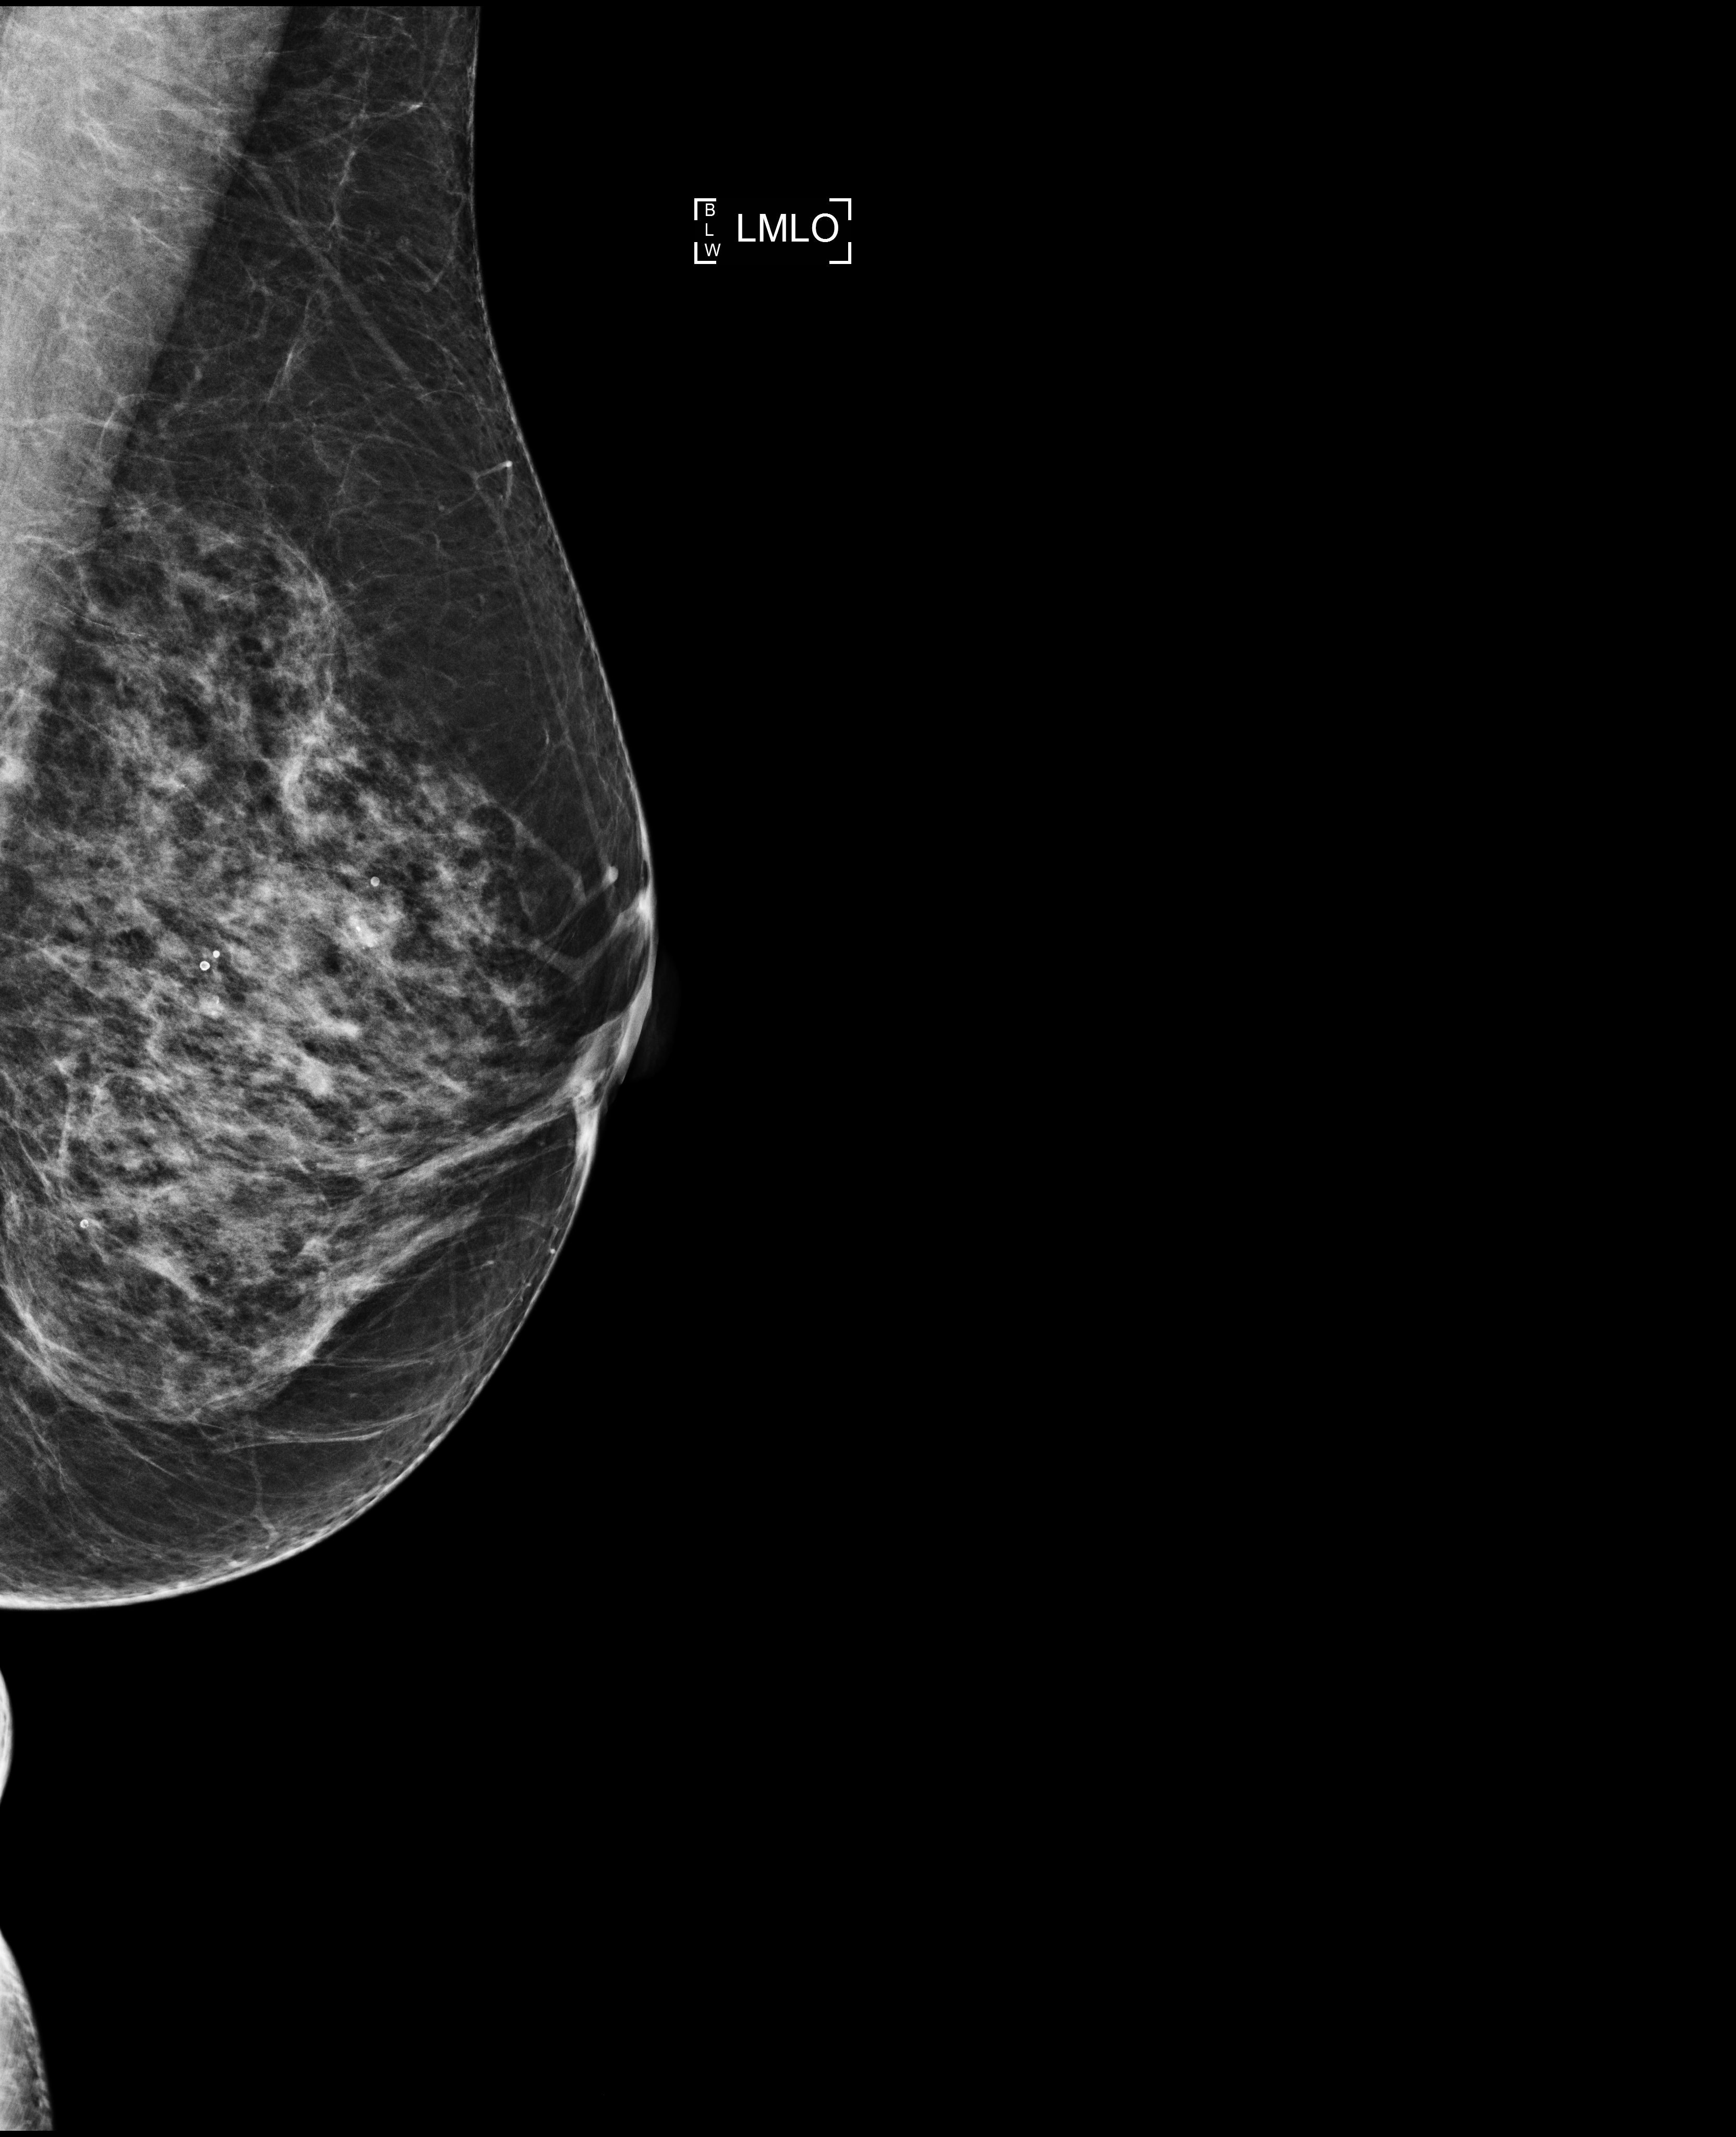
Digital mammogram (FFDM); left breast; medio-lateral oblique projection; screening examination; compressed breast thickness 60 mm. Female patient, age 60 years.
- BI-RADS breast density category at the screening exam (both breasts, scale 1–4): 3
- final BI-RADS category for the screening round (tomosynthesis exam, both breasts): category 2
- recall: no recall after this screen